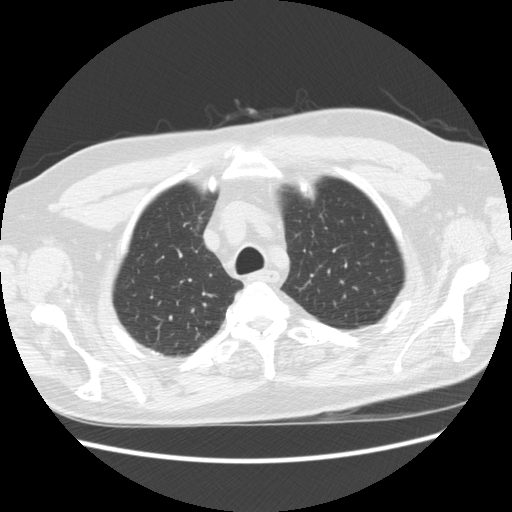
Low-dose screening chest CT, axial slice, baseline annual screen, lung window (W 1500 / L -600 HU), 2.5 mm slice thickness. Male, age 66 years at enrolment. Former smoker at enrolment.
Lesion marked by an expert reader, bounding box (x1, y1, x2, y2) in pixels: (163, 207, 214, 241). Screening reader's record for this exam: no non-calcified nodule ≥4 mm recorded. Official screen result: negative screen, significant abnormalities not suspicious for lung cancer. Later outcome: lung cancer diagnosed 951 days after this screen (after the third annual screen) — bronchiolo-alveolar adenocarcinoma, NOS, right upper lobe, moderately differentiated (G2), stage IA (AJCC 6th edition), 12 mm at pathology.